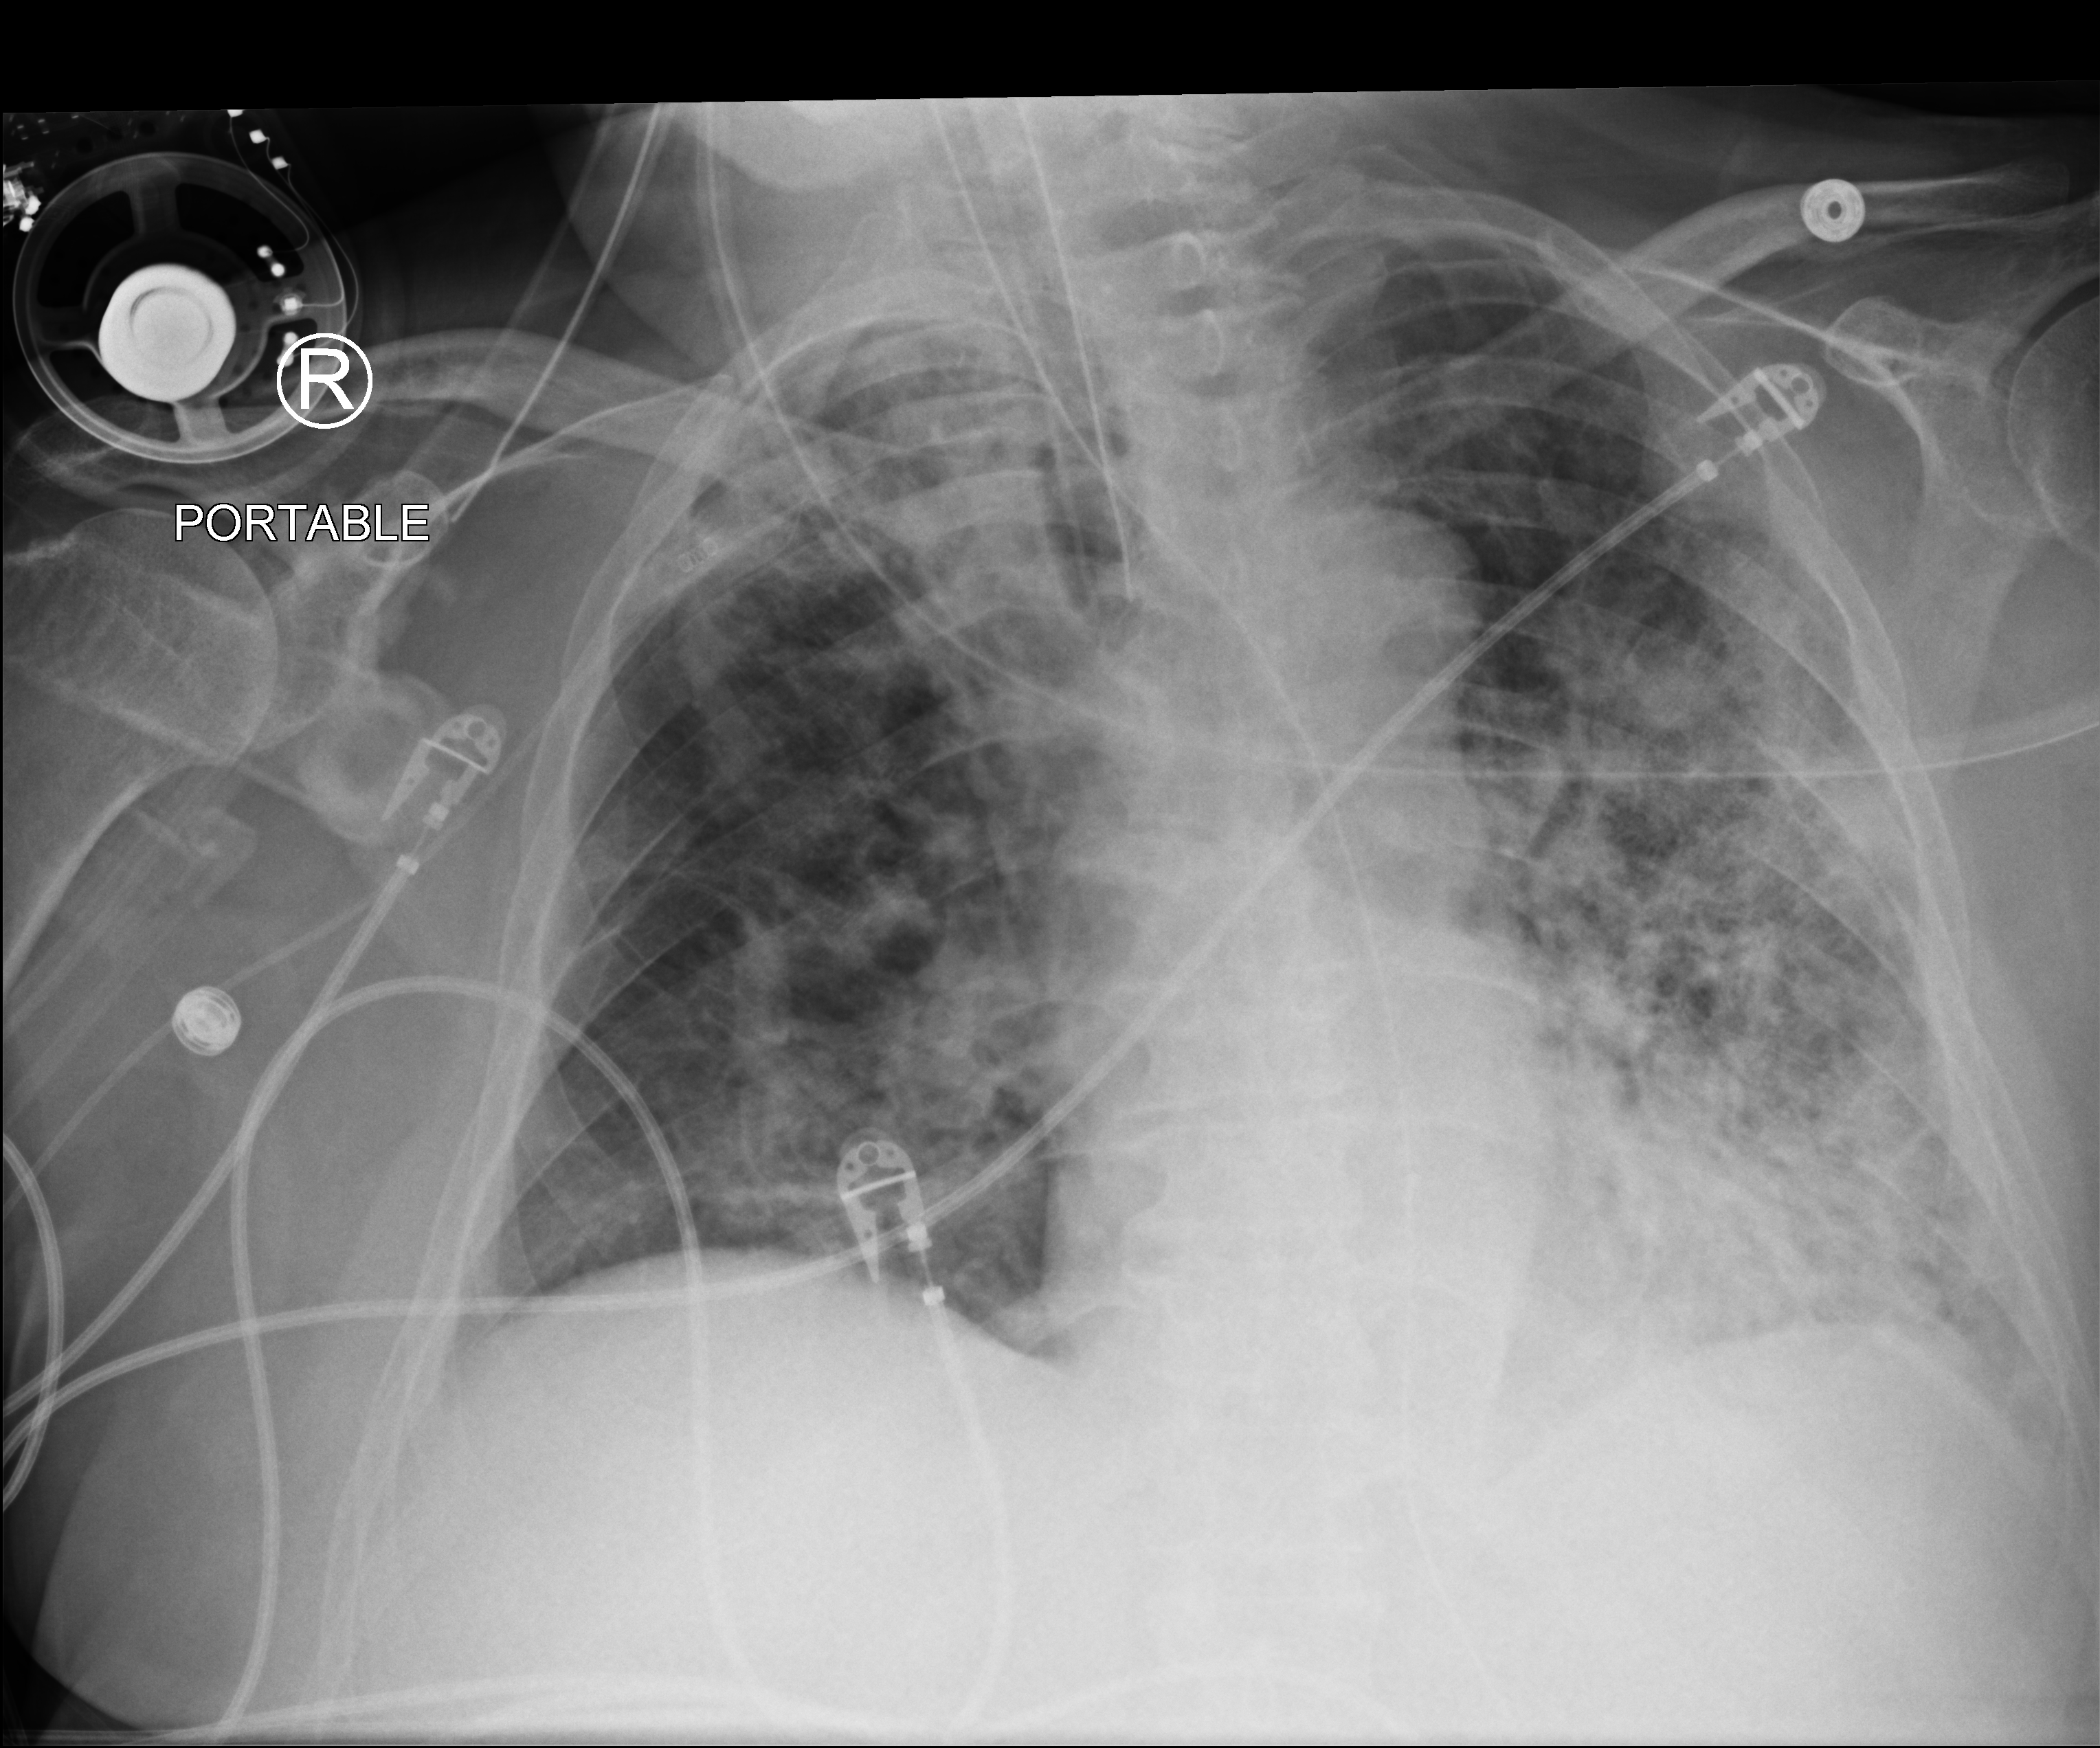
Portable chest radiograph; anteroposterior (AP) projection. Male patient hospitalised with COVID-19, age 60–74 years.
Admission-level facts for this patient (not findings on this image; timing relative to this image not recorded): length of hospital stay: 24 days.